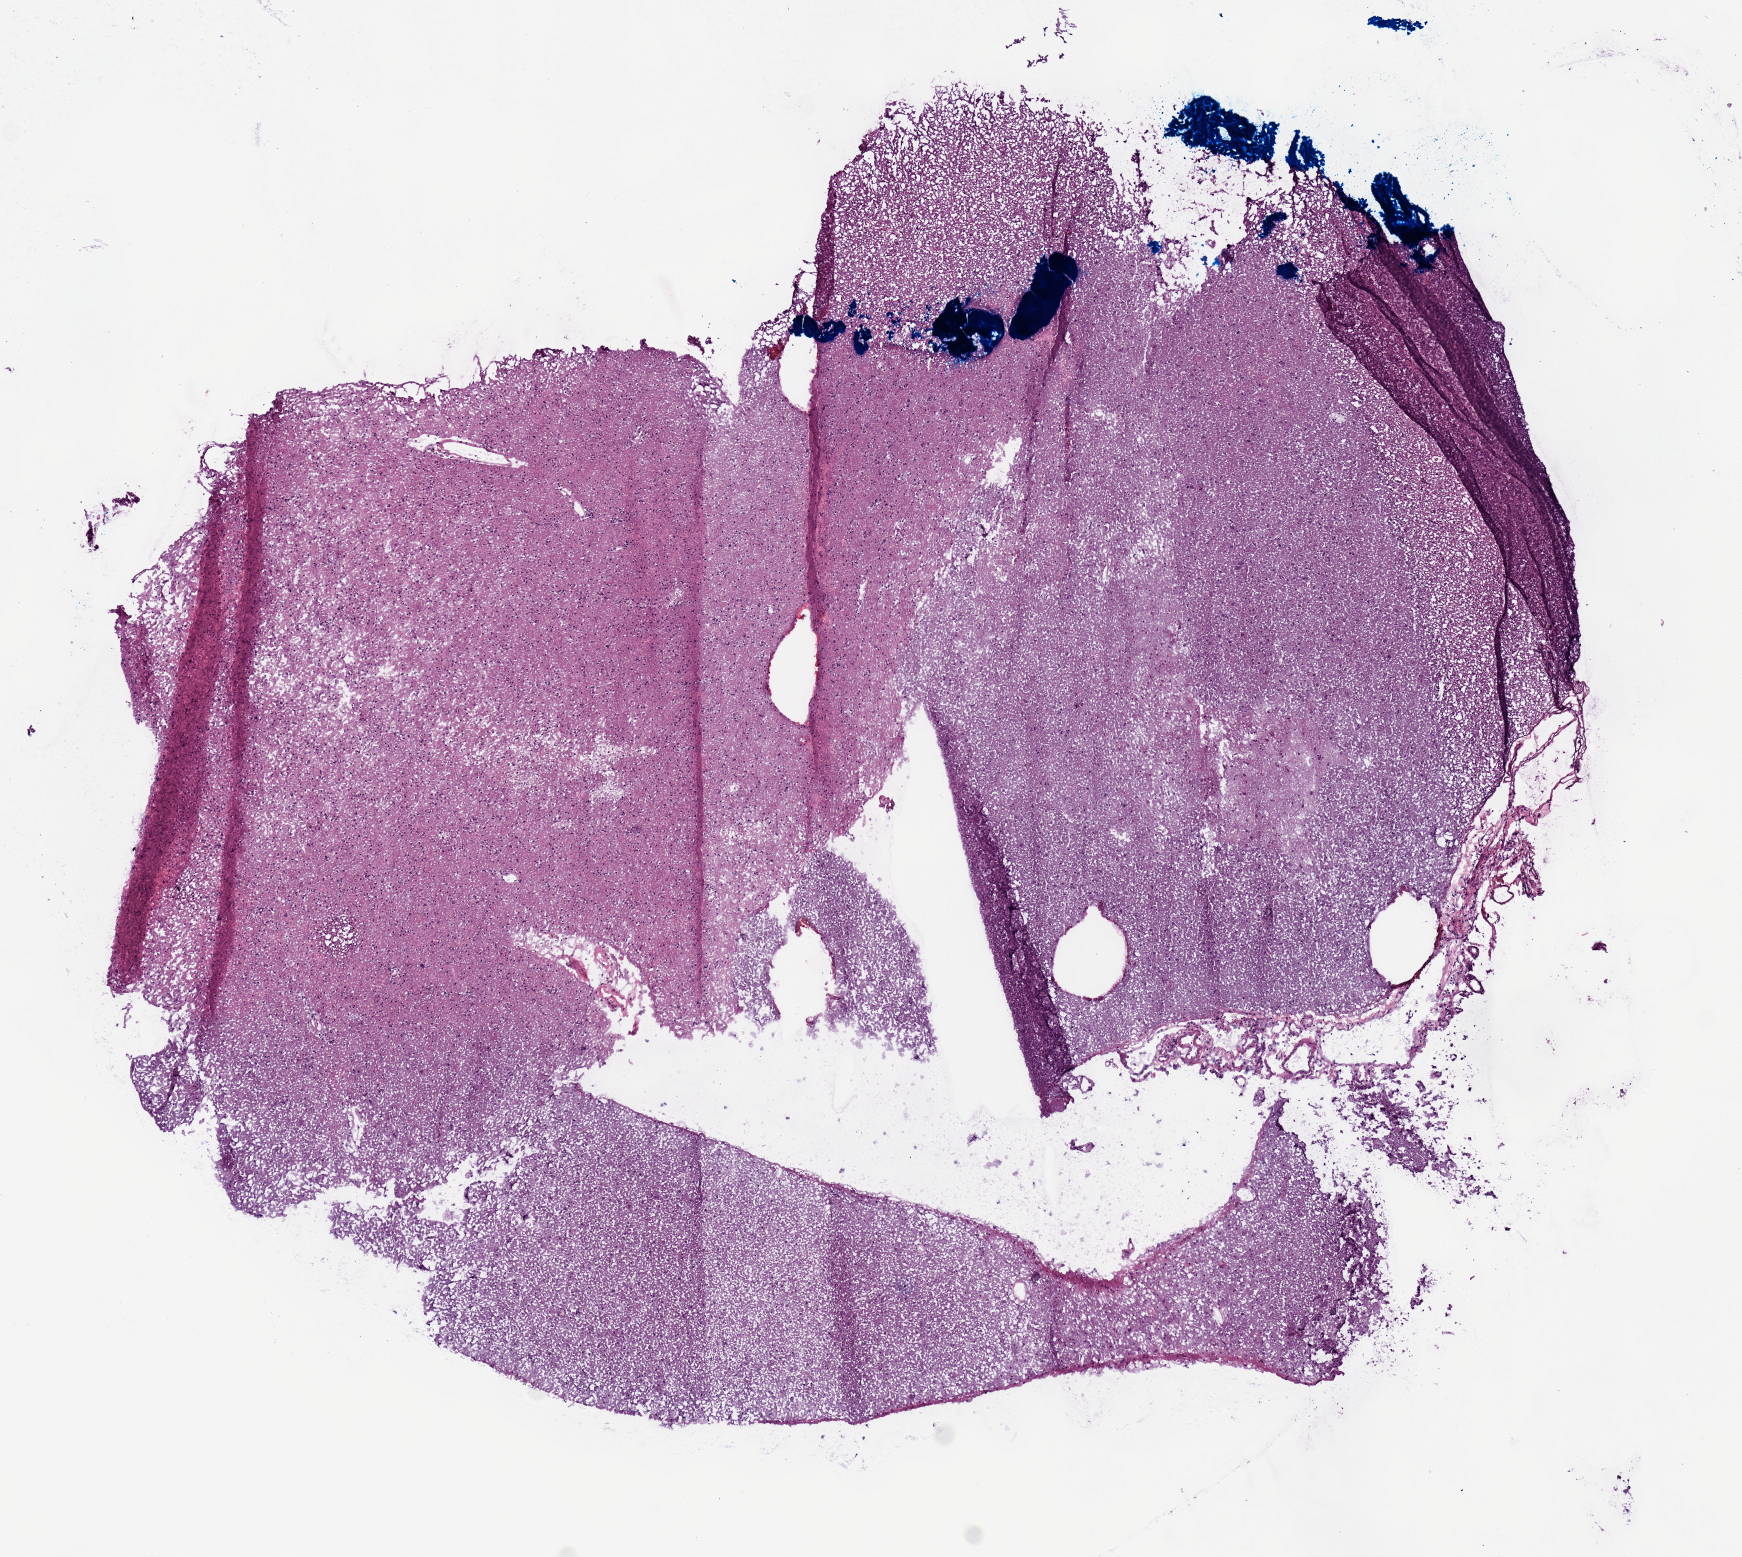
H&E whole-slide image — whole scanned area (about 6.9 x 6.2 mm, slide scanned at 20x) shown as a low-resolution overview; frozen section from the top of the tissue portion; brain, primary tumour sample. Female, age 49 years at initial diagnosis. Histologic grade: G2 (moderately differentiated). Composition of this section per pathologist review: tumour nuclei 55%, necrosis 0%.
Diagnosis: Mixed glioma (cerebrum). Laterality: right.